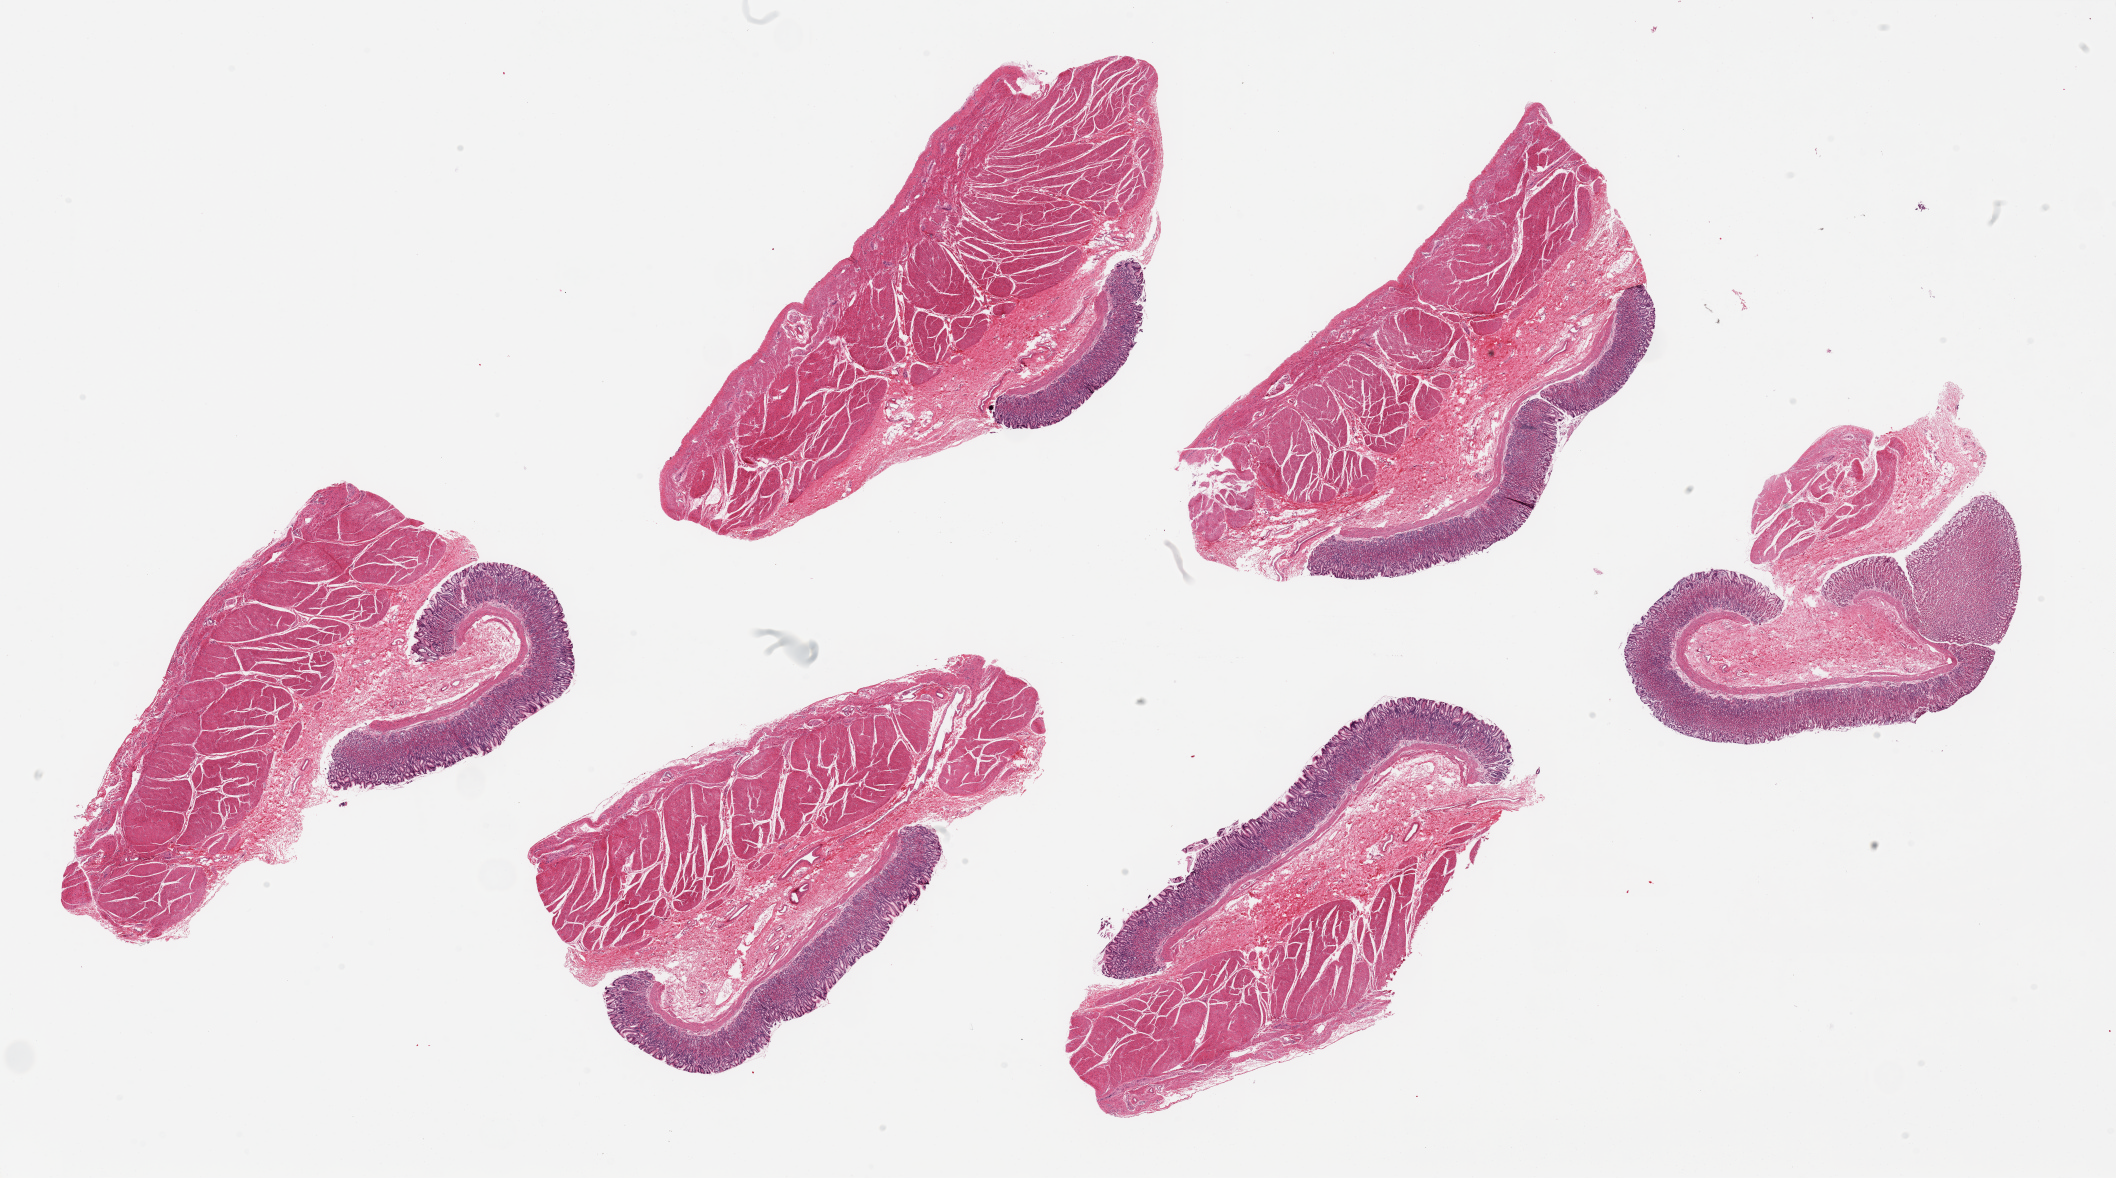
Whole-slide image, hematoxylin and eosin (H&E) stain, brightfield — whole scanned area (about 33.5 x 18.6 mm, from a 20x scan) shown as a low-resolution overview, PAXgene-fixed paraffin-embedded (PFPE) section, target tissue: stomach, donor tissue sample.
Review note (as recorded): 6 pieces up to 8x5 mm; well preserved oxyntic mucosa with slight surface sloughing.